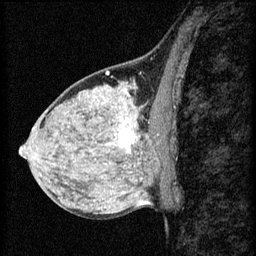
Breast MRI (dynamic contrast-enhanced), one sagittal slice. Position 32 of 60 along the scan axis. 3 images stored at this slice position (order not interpretable as contrast timing). 1.5 T. TE 4.2 ms, TR 8.2 ms. 2 mm slice thickness. 256 × 256 image matrix, field of view 180 × 180 mm. Female patient, age 40 years.
Structures marked on this image (semi-automatic segmentation, software-assisted and operator-edited):
- analysis volume of interest (the breast-tissue region the enhancement analysis was run in; not a lesion): bounding box <108,108,167,159> (left, top, right, bottom; pixels)
- tumour enhancement mask (voxels above the 70 % enhancement threshold inside the analysis volume of interest): <108,118,159,153>